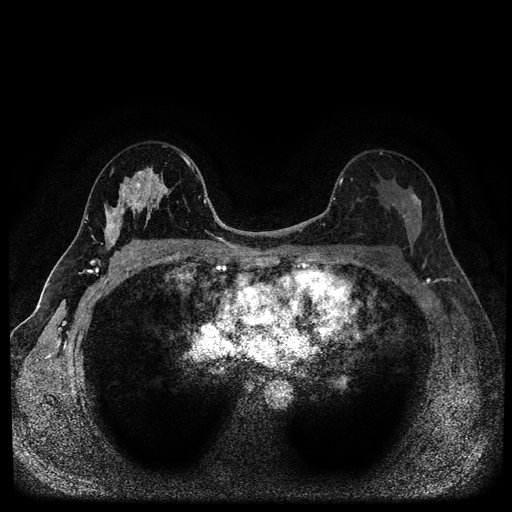
Breast MRI (dynamic contrast-enhanced, multi-phase), one axial slice; position 62 of 116 along the scan axis; dynamic contrast-enhanced series, time point 2 of 5 at this slice position (early post-contrast); 1.5 T; TE 2.7 ms, TR 5.4 ms; 2 mm slice thickness; 512 × 512 image matrix. Patient: female, 49 years.
Annotated regions visible in this slice (semi-automatically segmented with operator editing):
- breast lesion (labelled benign in the annotation): bounding box <102,165,170,246> (left, top, right, bottom; pixels)